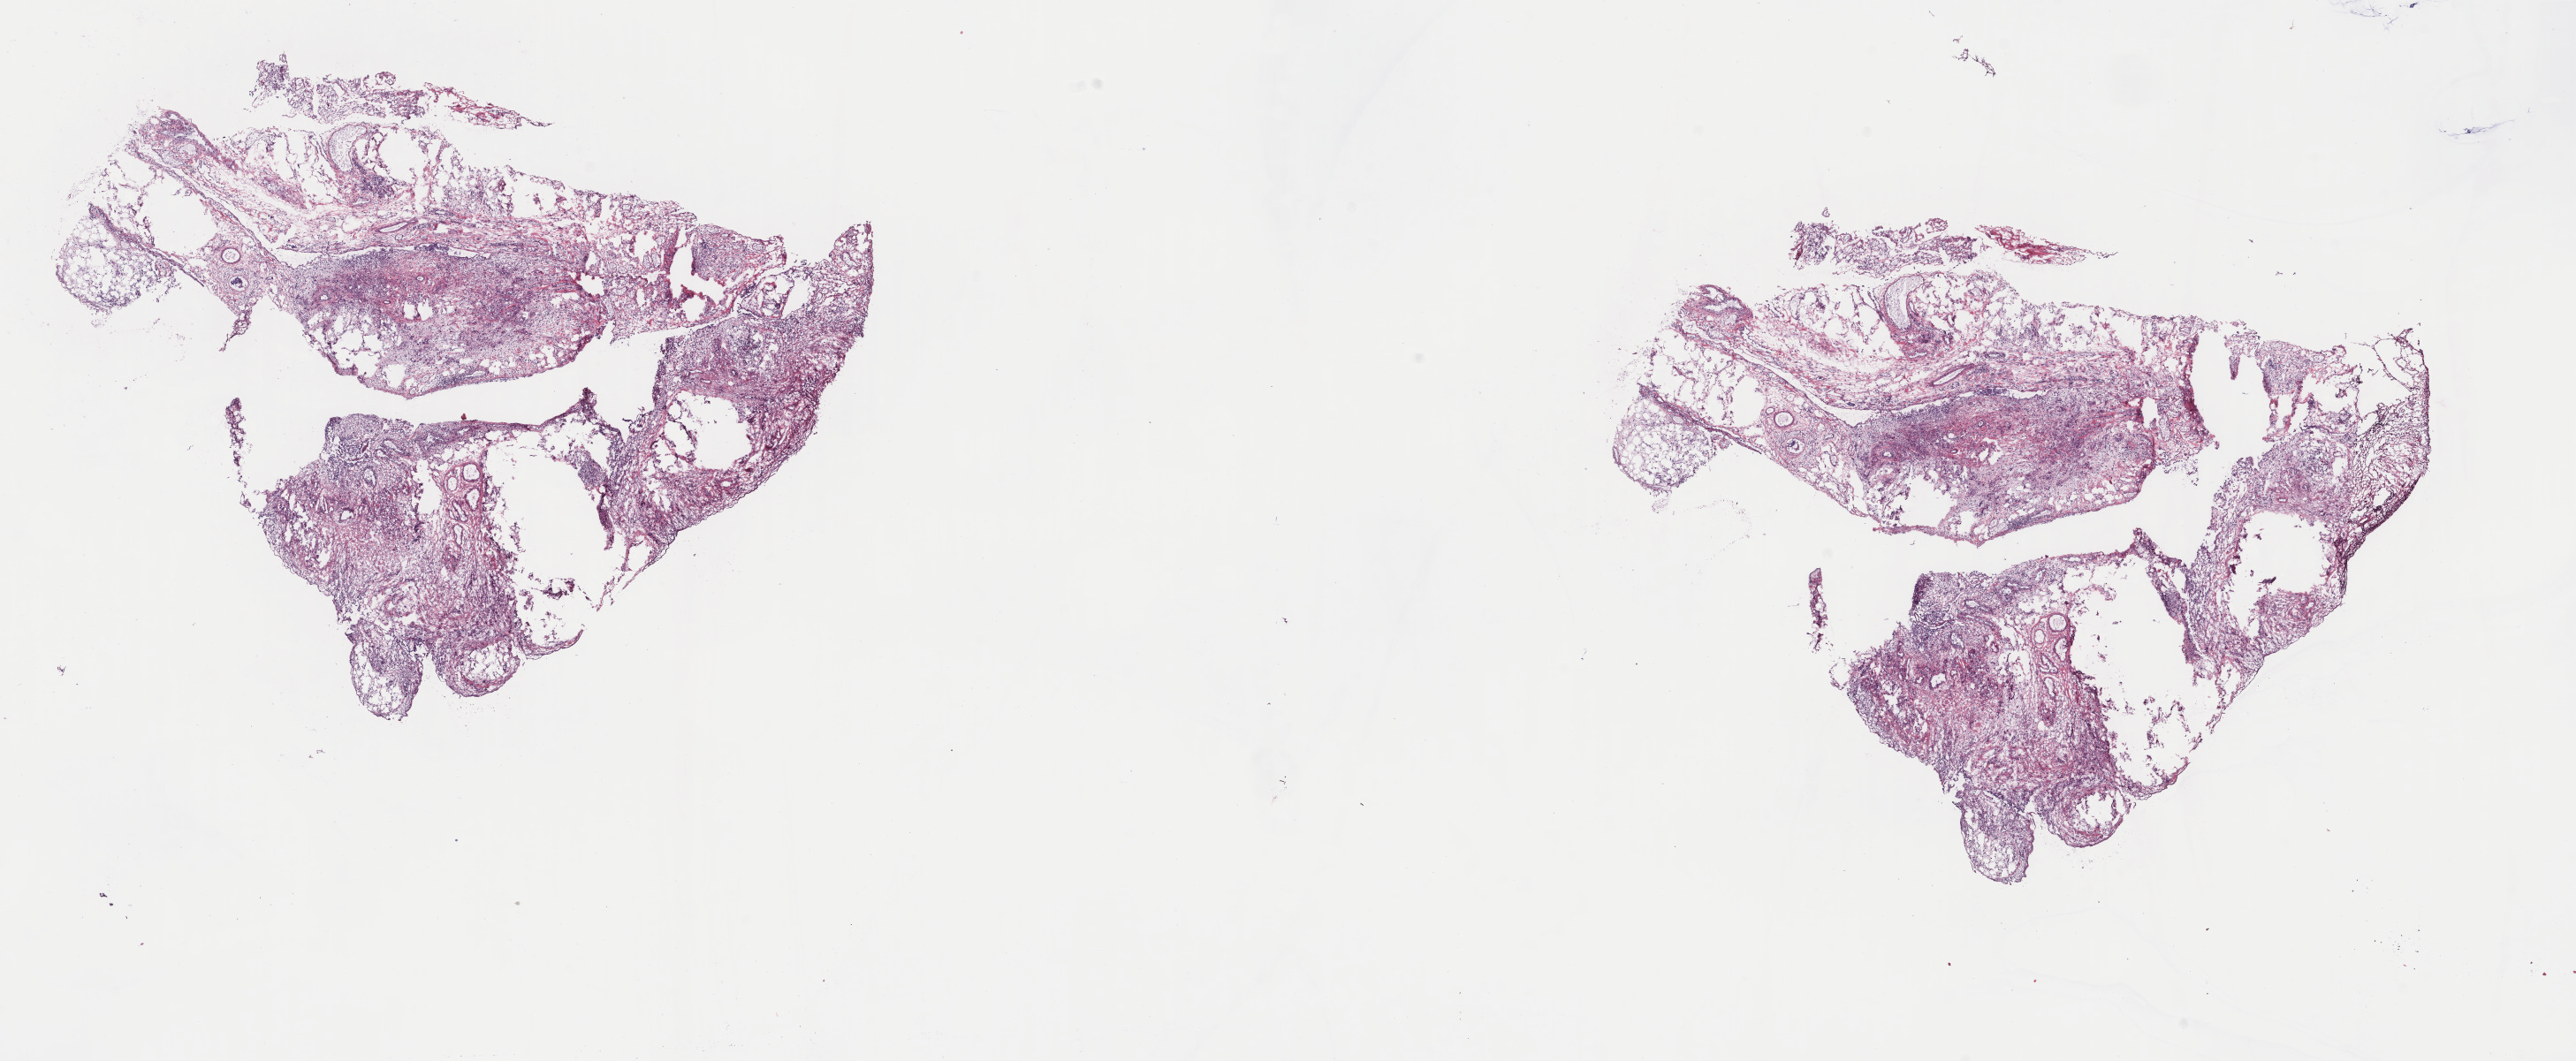
Hematoxylin and eosin (H&E) stained whole-slide image, low-resolution overview of the scanned area, about 23.1 x 9.5 mm (slide scanned at 40x). Frozen section from the top of the tissue portion. Stomach, primary tumour sample. Female, age 45 years at initial diagnosis. Histologic grade: G3 (poorly differentiated). Pathologist review of this section (percent, as recorded): tumour cells 100%, tumour nuclei 65%, normal cells 0%, stromal cells 0%, necrosis 0%. Inflammatory infiltration, as recorded: lymphocyte infiltration 2%, monocyte infiltration 0%, neutrophil infiltration 0%.
TNM: T4a N2 M0. AJCC pathologic stage: IIIB (7th edition). Diagnosis: Carcinoma, diffuse type (gastric antrum).